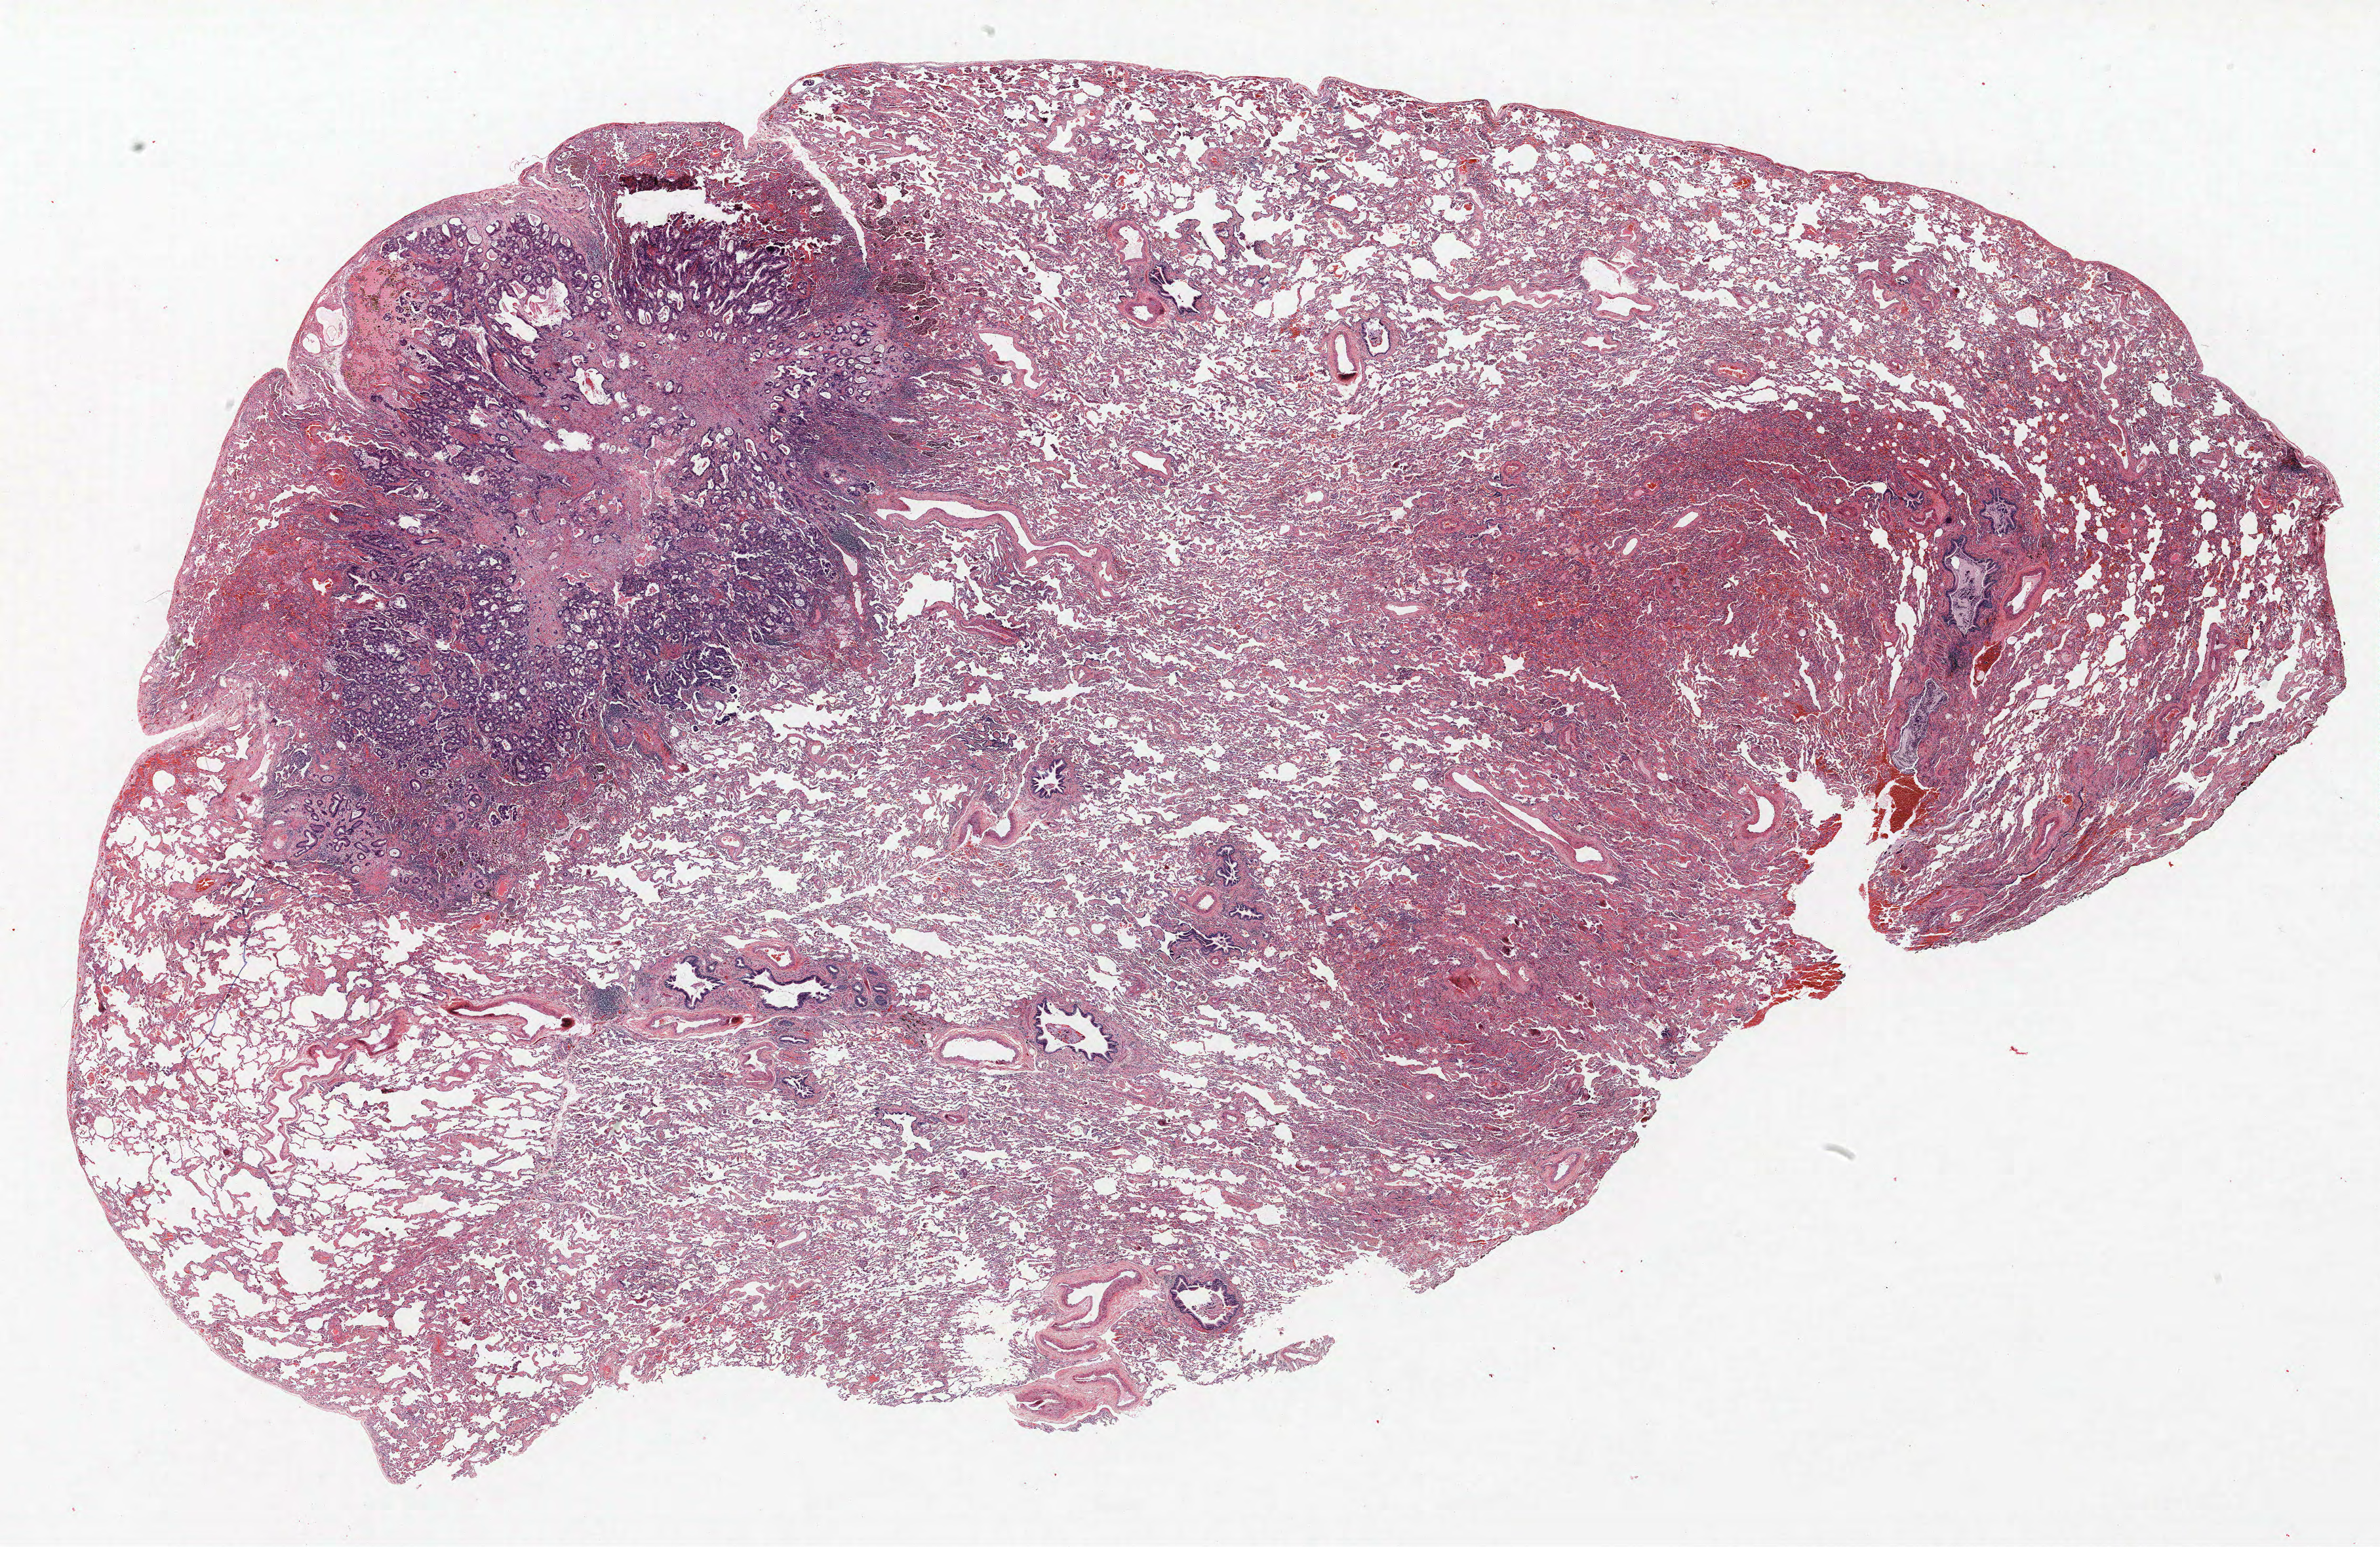
Hematoxylin and eosin (H&E) stained whole-slide image — whole scanned area (about 29.0 x 18.9 mm, slide scanned at 40x) shown as a low-resolution overview; FFPE section; lung tissue. Female, age 63 at enrolment. Current smoker at enrolment. Grade: moderately differentiated (G2).
Primary tumour location (clinical record): left lower lobe. Tumour size (pathology): 8 mm. Stage (AJCC 6th edition): IIIA. Participant's lung-cancer diagnosis: Adenocarcinoma, NOS.